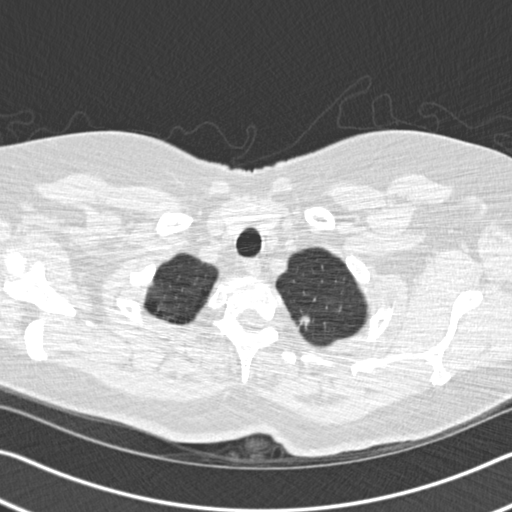
Chest CT (low-dose screening protocol), one axial image. Baseline screening round. Lung window (W 1500 / L -600 HU). Standard (soft-tissue) reconstruction kernel (B30f). Slice 28 of 233 in the series. 512 × 512 image matrix, field of view 338 × 338 mm. Female participant, aged 60 years at enrolment. Former smoker at enrolment.
- Lesion marked by an expert reader, bounding box <282,304,324,343> (left, top, right, bottom; pixels).
- Screening reader's record for this exam: no non-calcified nodule ≥4 mm recorded.
- Official screen result: negative screen, minor abnormalities not suspicious for lung cancer.
- Participant outcome: lung cancer diagnosed 799 days after this screen (after the third annual screen) — non-small cell carcinoma, left upper lobe, poorly differentiated (G3), stage IB (AJCC 6th edition), 16 mm at pathology.